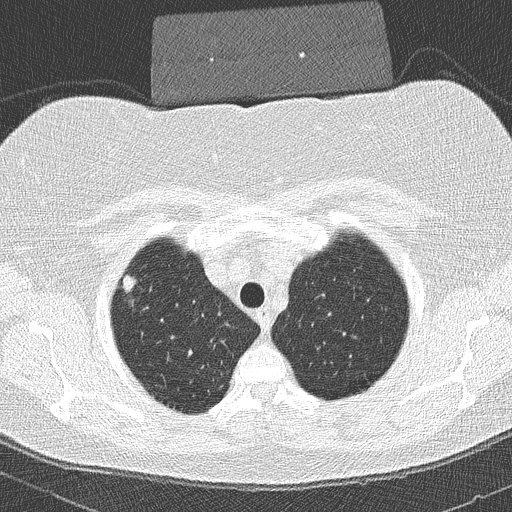
Low-dose screening chest CT, axial slice, second annual screen, lung window (W 1500 / L -600 HU), 120 kVp. Female participant, aged 58 years at enrolment. Former smoker at enrolment.
- Expert reader's lesion annotation, bounding box [x1, y1, x2, y2] px = [111, 270, 149, 309].
- The screening reader recorded 2 non-calcified nodules or masses ≥4 mm on this exam; which of them this box marks is not recorded.
- Official screen result: positive, other.